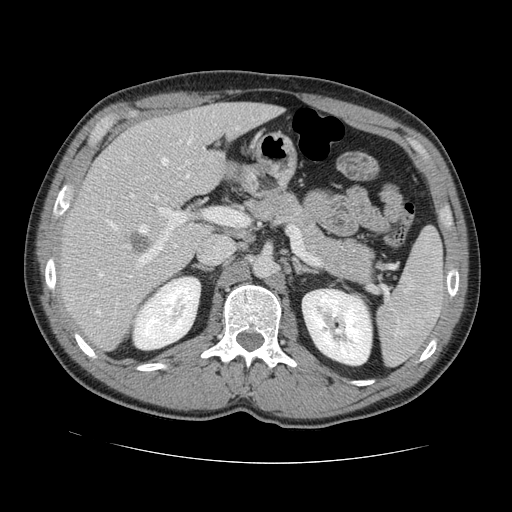
Contrast-enhanced abdominal CT, one axial slice. Slice 79 of 131 in the series (ordered by position). 120 kVp. Intravenous contrast given. Soft-tissue window (W 400 / L 40 HU). 512 × 512 image matrix, field of view 380 × 380 mm. Male patient, age 40 years. Case-level facts recorded for this patient, not image findings: diagnosis: colorectal cancer liver metastases, imaged before liver resection.
Structures marked on this image (outlined manually by an expert reader):
- hepatic veins: bounding box [x1, y1, x2, y2] px = [96, 137, 191, 314]
- liver: [62, 104, 278, 349]
- planned liver remnant (the part of the liver to remain after resection): [105, 103, 277, 199]
- portal vein (with intrahepatic branches): [125, 194, 234, 280]
- liver metastasis: [130, 232, 152, 256]